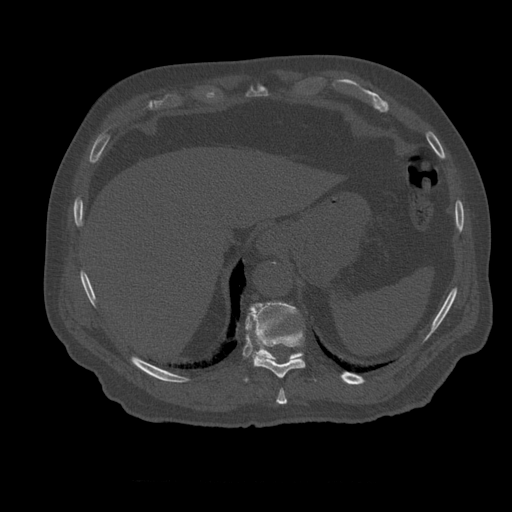
CT including the spine, one axial slice. Position 297 of 399 along the scan axis. Reconstruction kernel STANDARD. 120 kVp. Bone window (W 1800 / L 400 HU). 1.25 mm slice thickness. 512 × 512 image matrix. Patient age 73 years. Case-level facts recorded for this patient, not image findings: primary cancer: prostate; vertebrae with lytic lesions (as recorded): L2.
Annotated regions visible in this slice (semi-automatic segmentation, software-assisted and operator-edited):
- T10 vertebra: bounding box <245,331,306,382> (left, top, right, bottom; pixels)
- T11 vertebra: <246,302,303,361>
- T9 vertebra: <277,389,288,405>